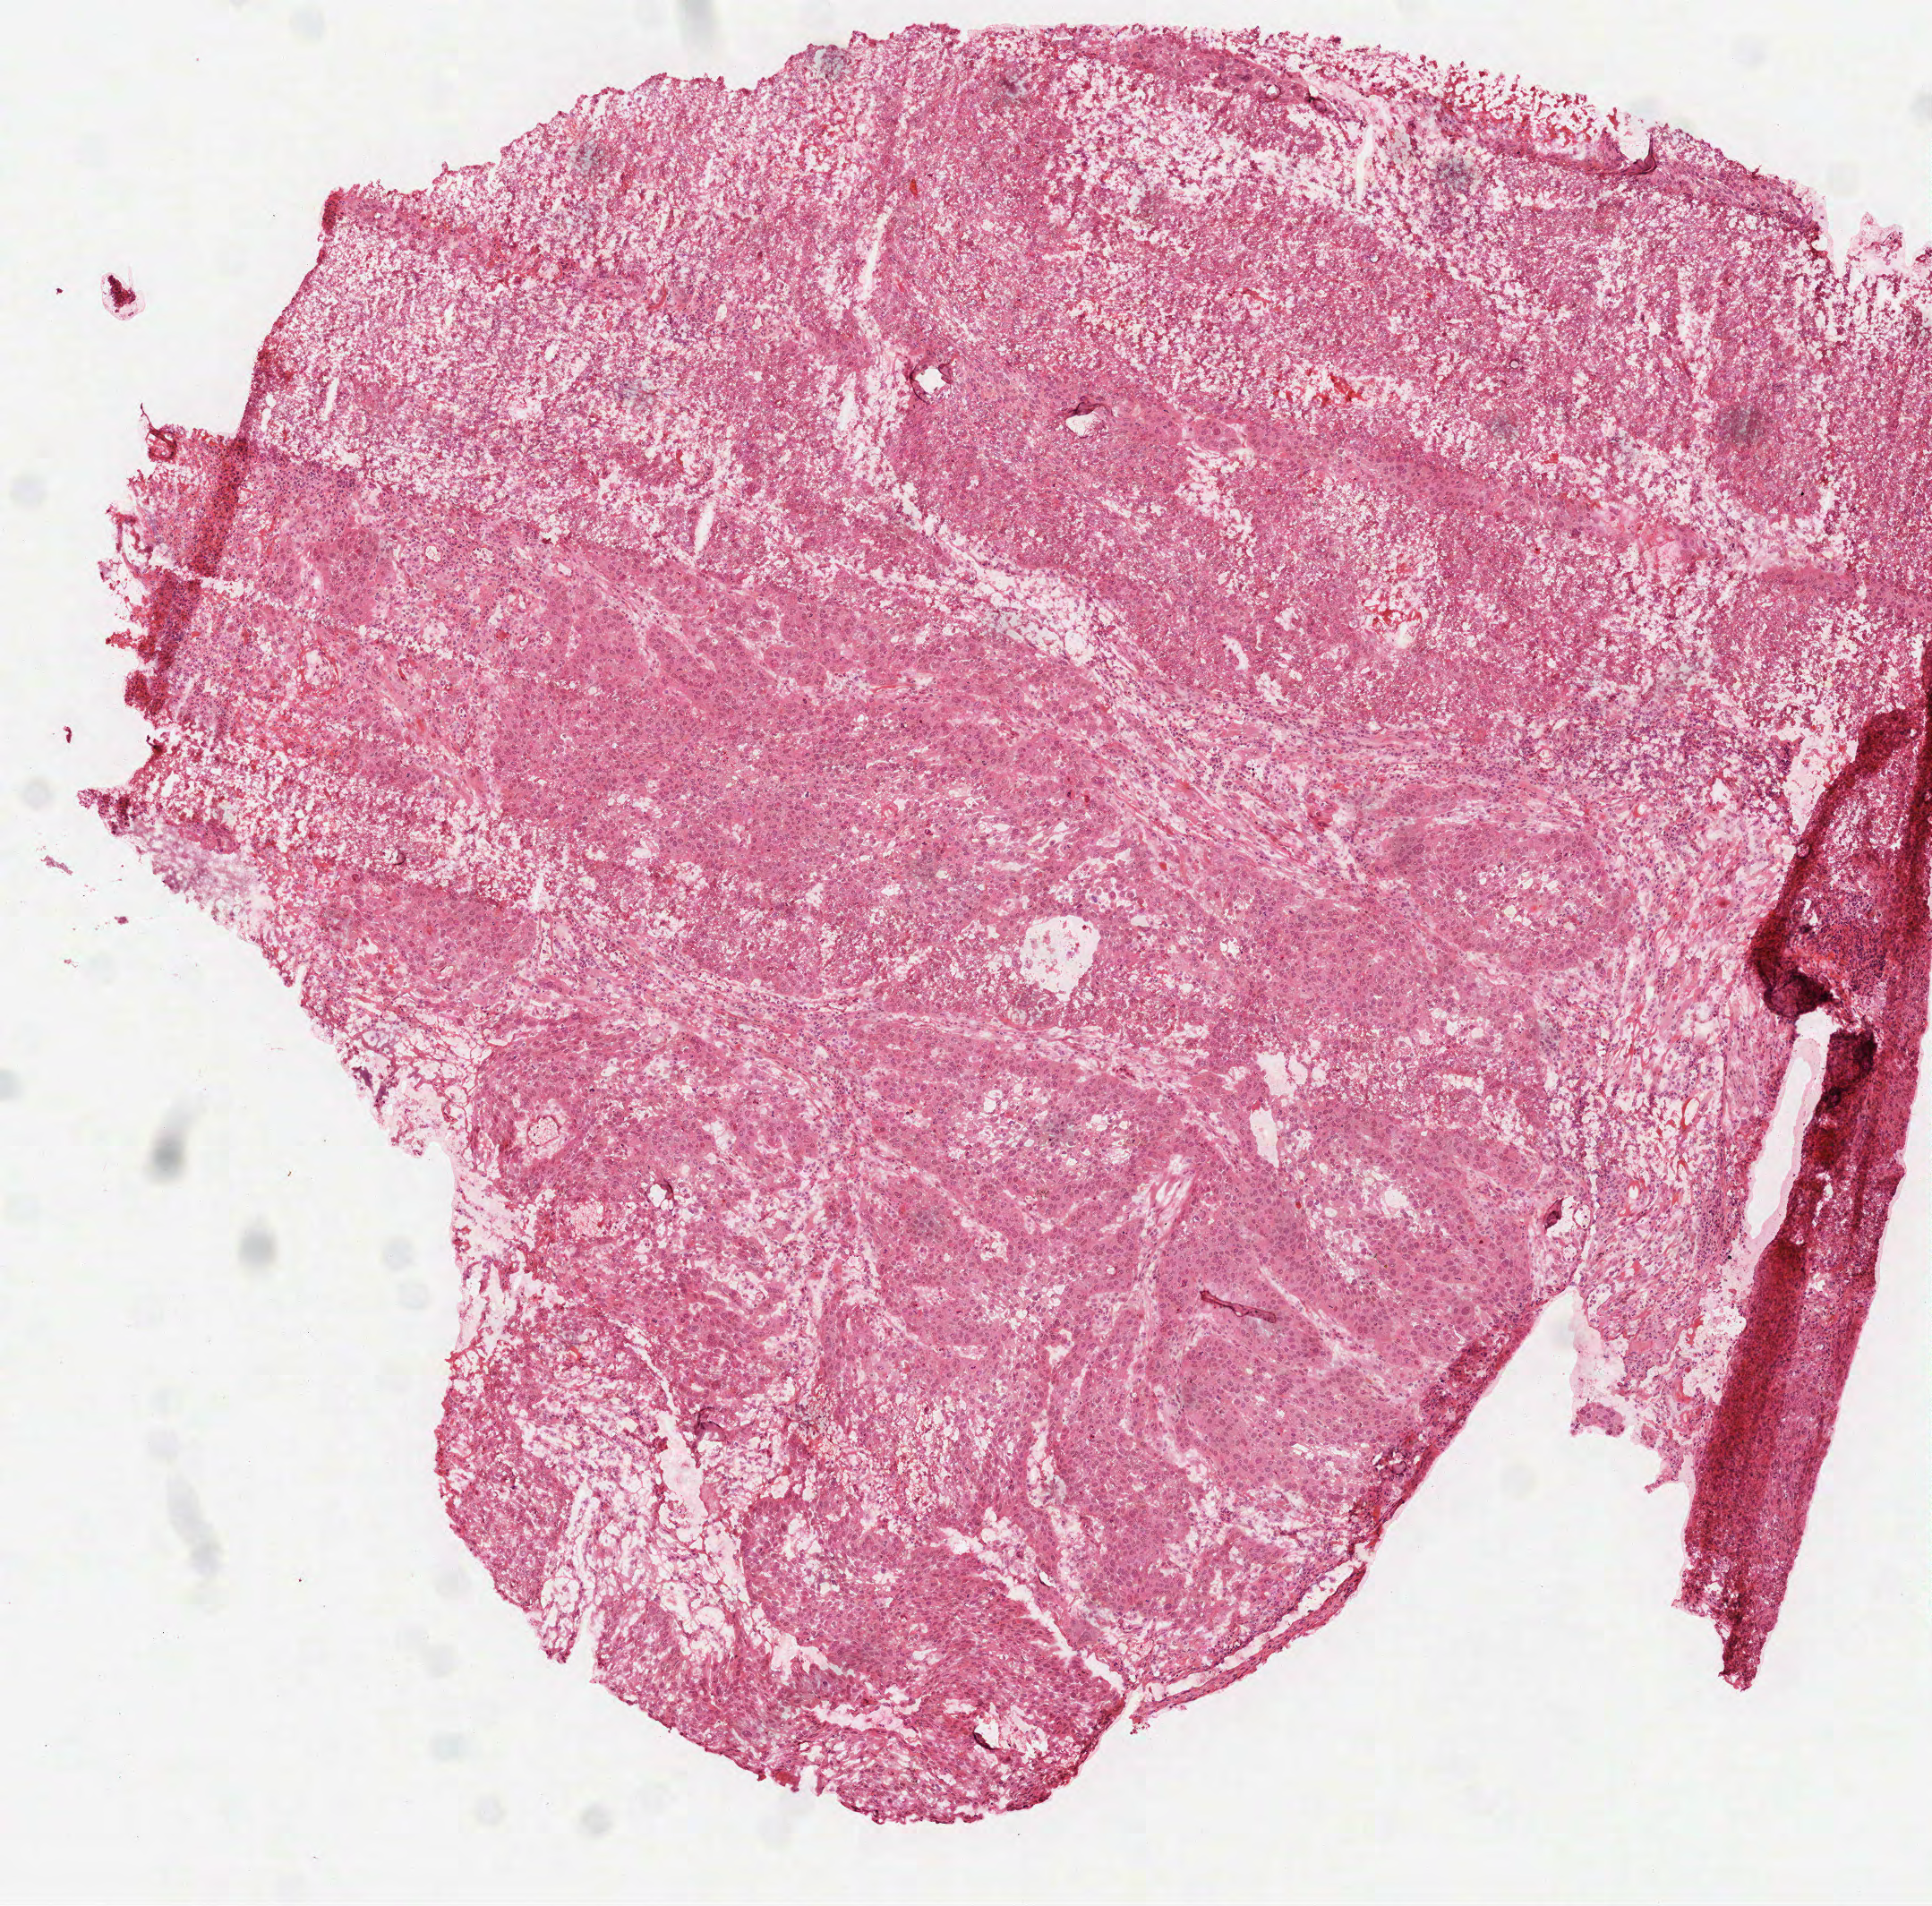
H&E whole-slide image — shown as a low-resolution overview of the whole scanned area (about 4.4 x 4.3 mm, slide scanned at 40x), frozen section, head and neck, primary tumour sample. Patient: male, age at initial diagnosis 50 years. Histologic grade: G2 (moderately differentiated). Composition of this section per pathologist review: tumour cells 82%, tumour nuclei 75%, normal cells 0%, stromal cells 18%, necrosis 0%.
Diagnosis: Squamous cell carcinoma, NOS (tongue, NOS). TNM: T2 N0. AJCC pathologic stage: II.